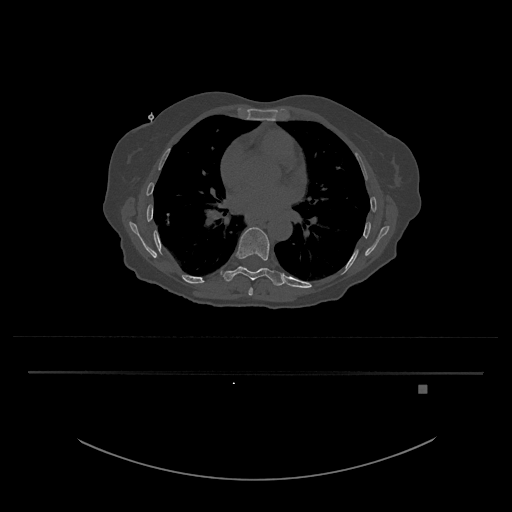
CT including the spine, one axial slice; position 760 of 797 along the scan axis; reconstruction kernel Br40s/3; 120 kVp; bone window (W 1800 / L 400 HU); 0.5 mm slice thickness; 512 × 512 image matrix, field of view 500 × 500 mm. Female patient, age 57 years. Case-level facts recorded for this patient, not image findings: primary cancer: cervical.
Outlined on this slice (semi-automatically segmented with operator editing):
- T10 vertebra: box from (x=259, y=268) to (x=262, y=270) px
- T8 vertebra: (x=248, y=287)–(x=253, y=296)
- T9 vertebra: (x=223, y=227)–(x=284, y=286)